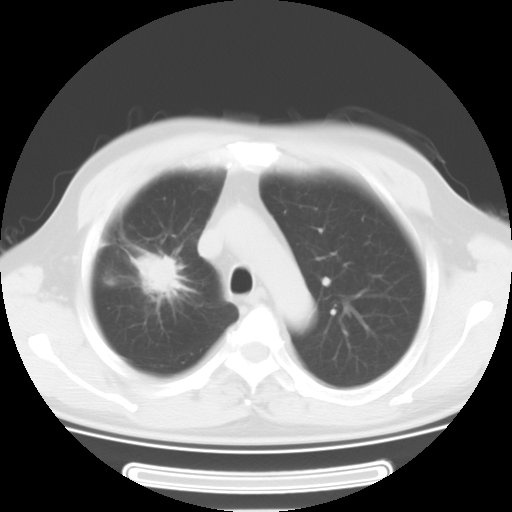
Chest CT, one axial slice. Position 22 of 29 along the scan axis. Reconstruction kernel STANDARD. Lung window (W 1500 / L -600 HU). 512 × 512 image matrix, field of view 350 × 350 mm. Male patient, age 46 years. Case-level facts recorded for this patient, not image findings: clinical TNM (as recorded): T3 N0 M1b.
Outlined on this slice (rectangle marked by the reading radiologist):
- lung tumour (recorded histology: adenocarcinoma): box from (x=115, y=235) to (x=183, y=305) px